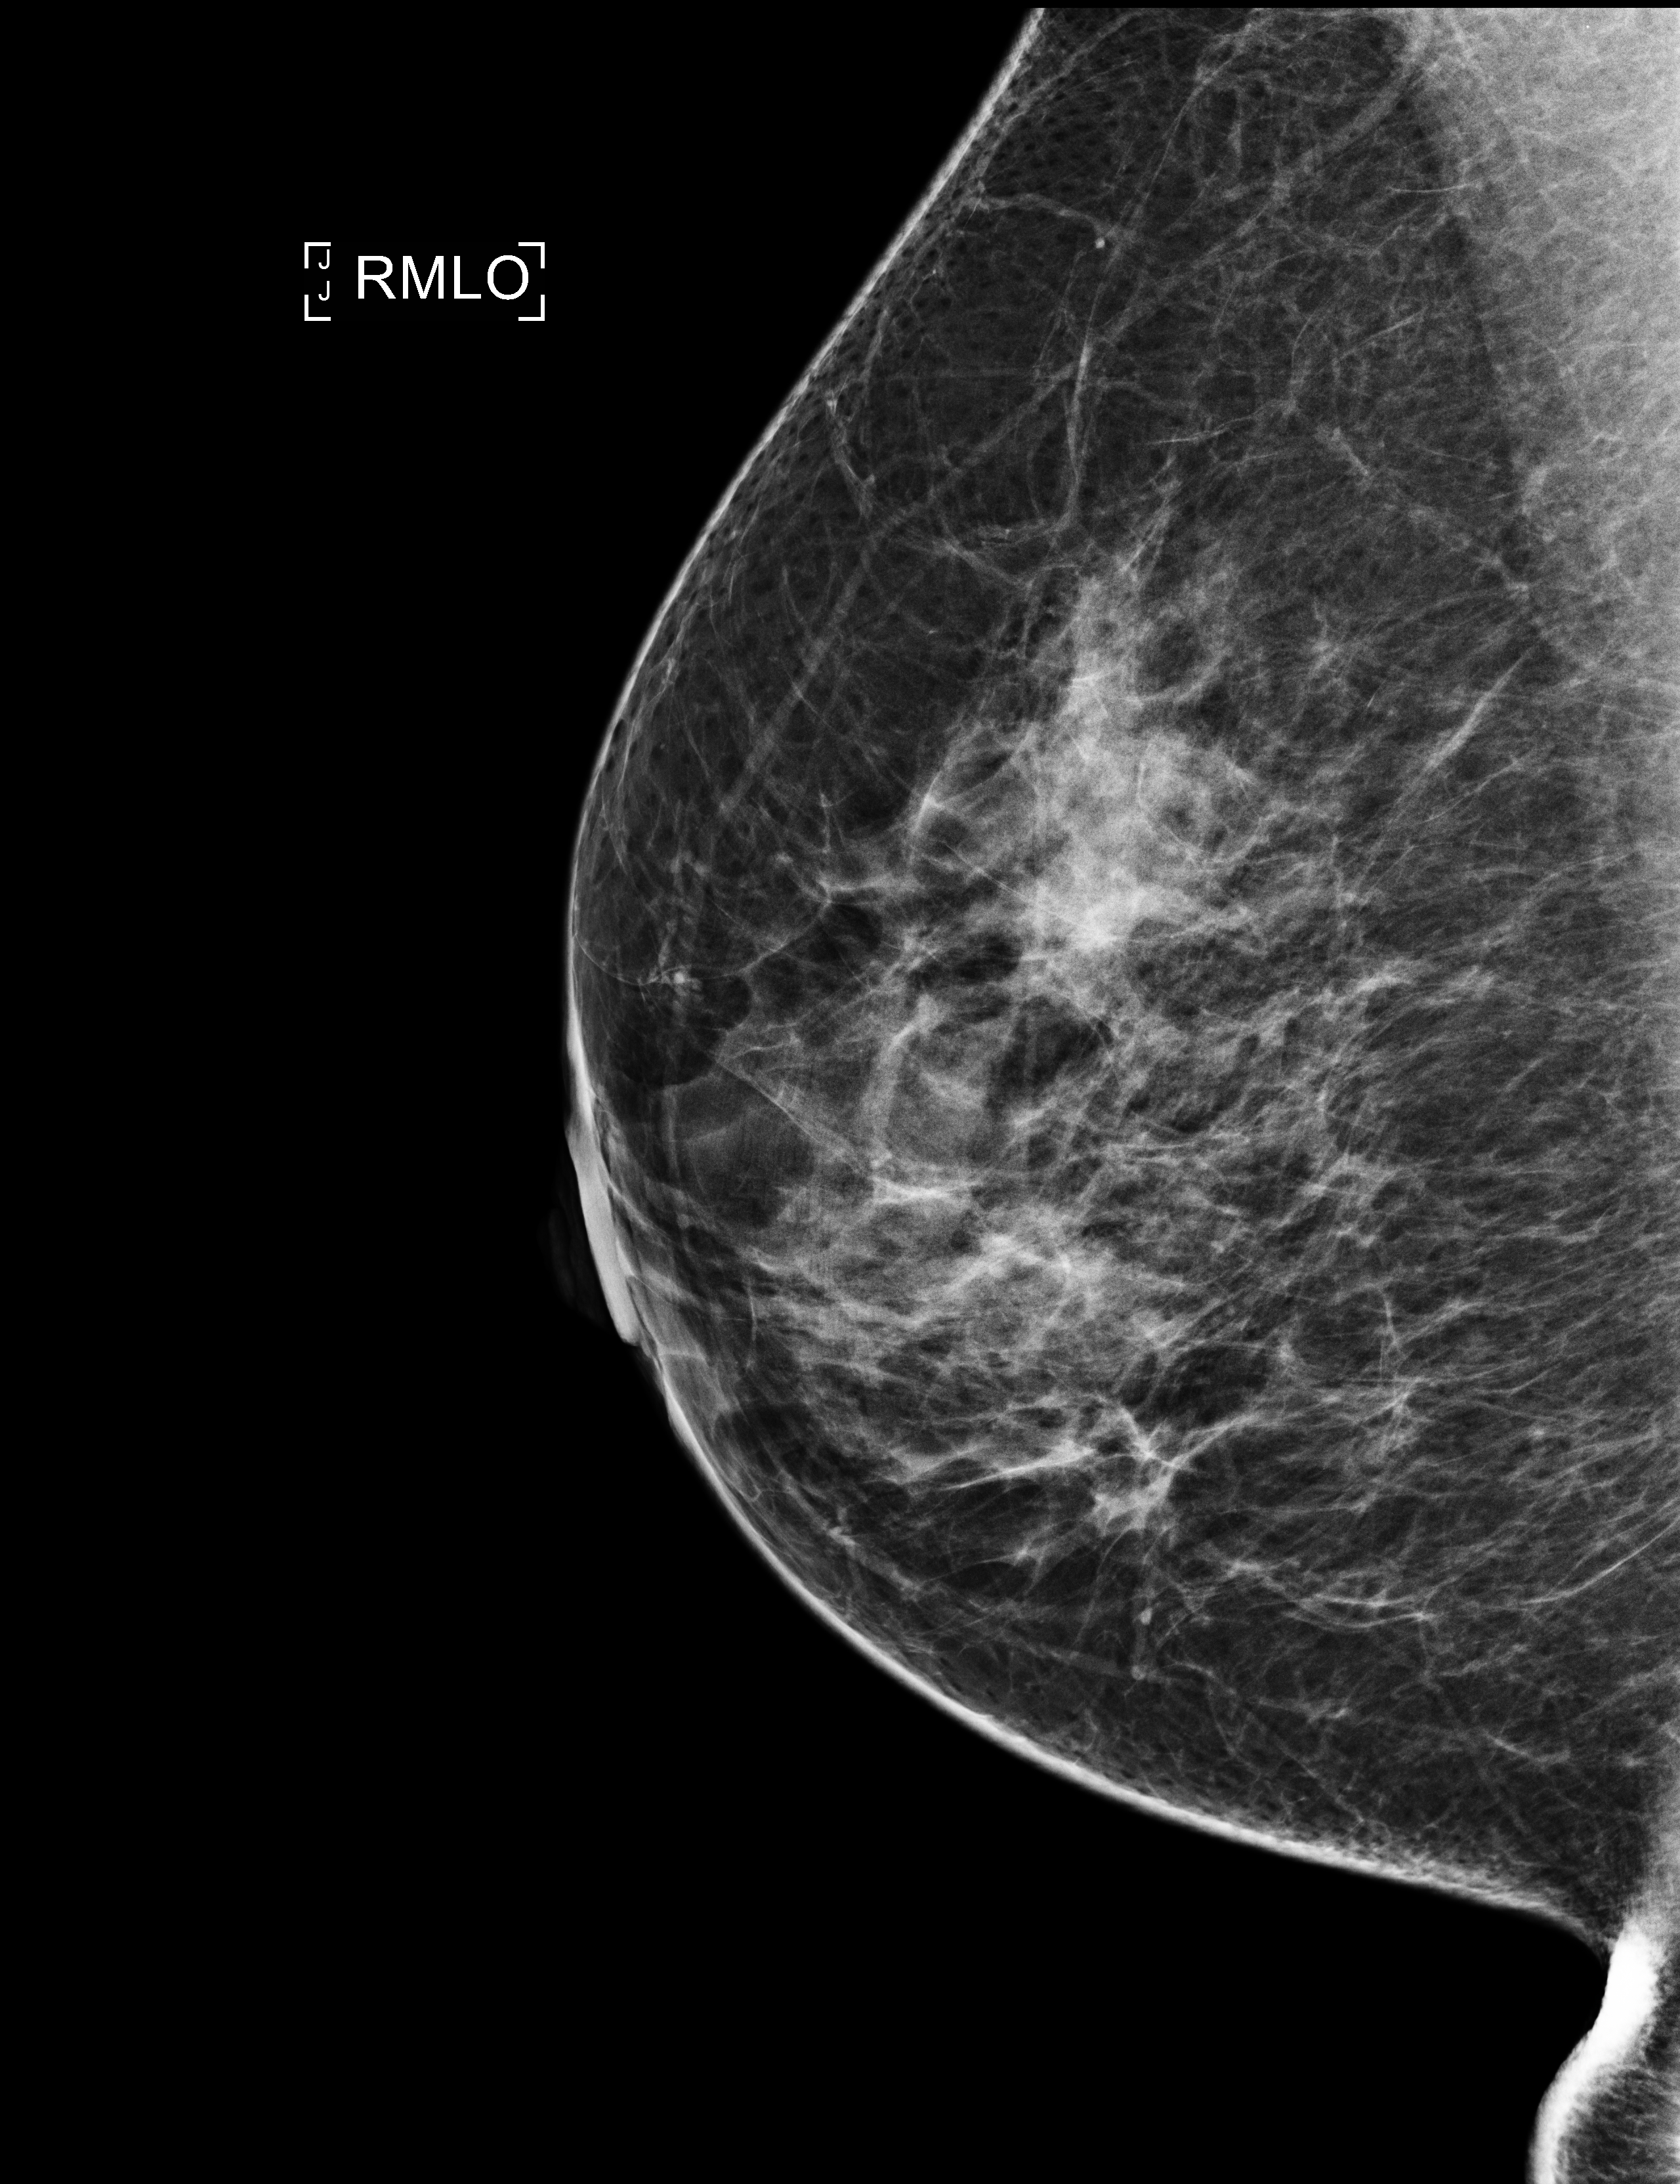
Full-field digital mammogram (FFDM), right breast, mediolateral oblique (MLO) view, screening examination, system: Selenia Dimensions. Patient: female, 53 years.
Breast density at the screening exam (both breasts): scattered fibroglandular densities (BI-RADS density category b). Final BI-RADS category for the screening round (tomosynthesis exam, both breasts): category 1. Recall: no recall after this screen.